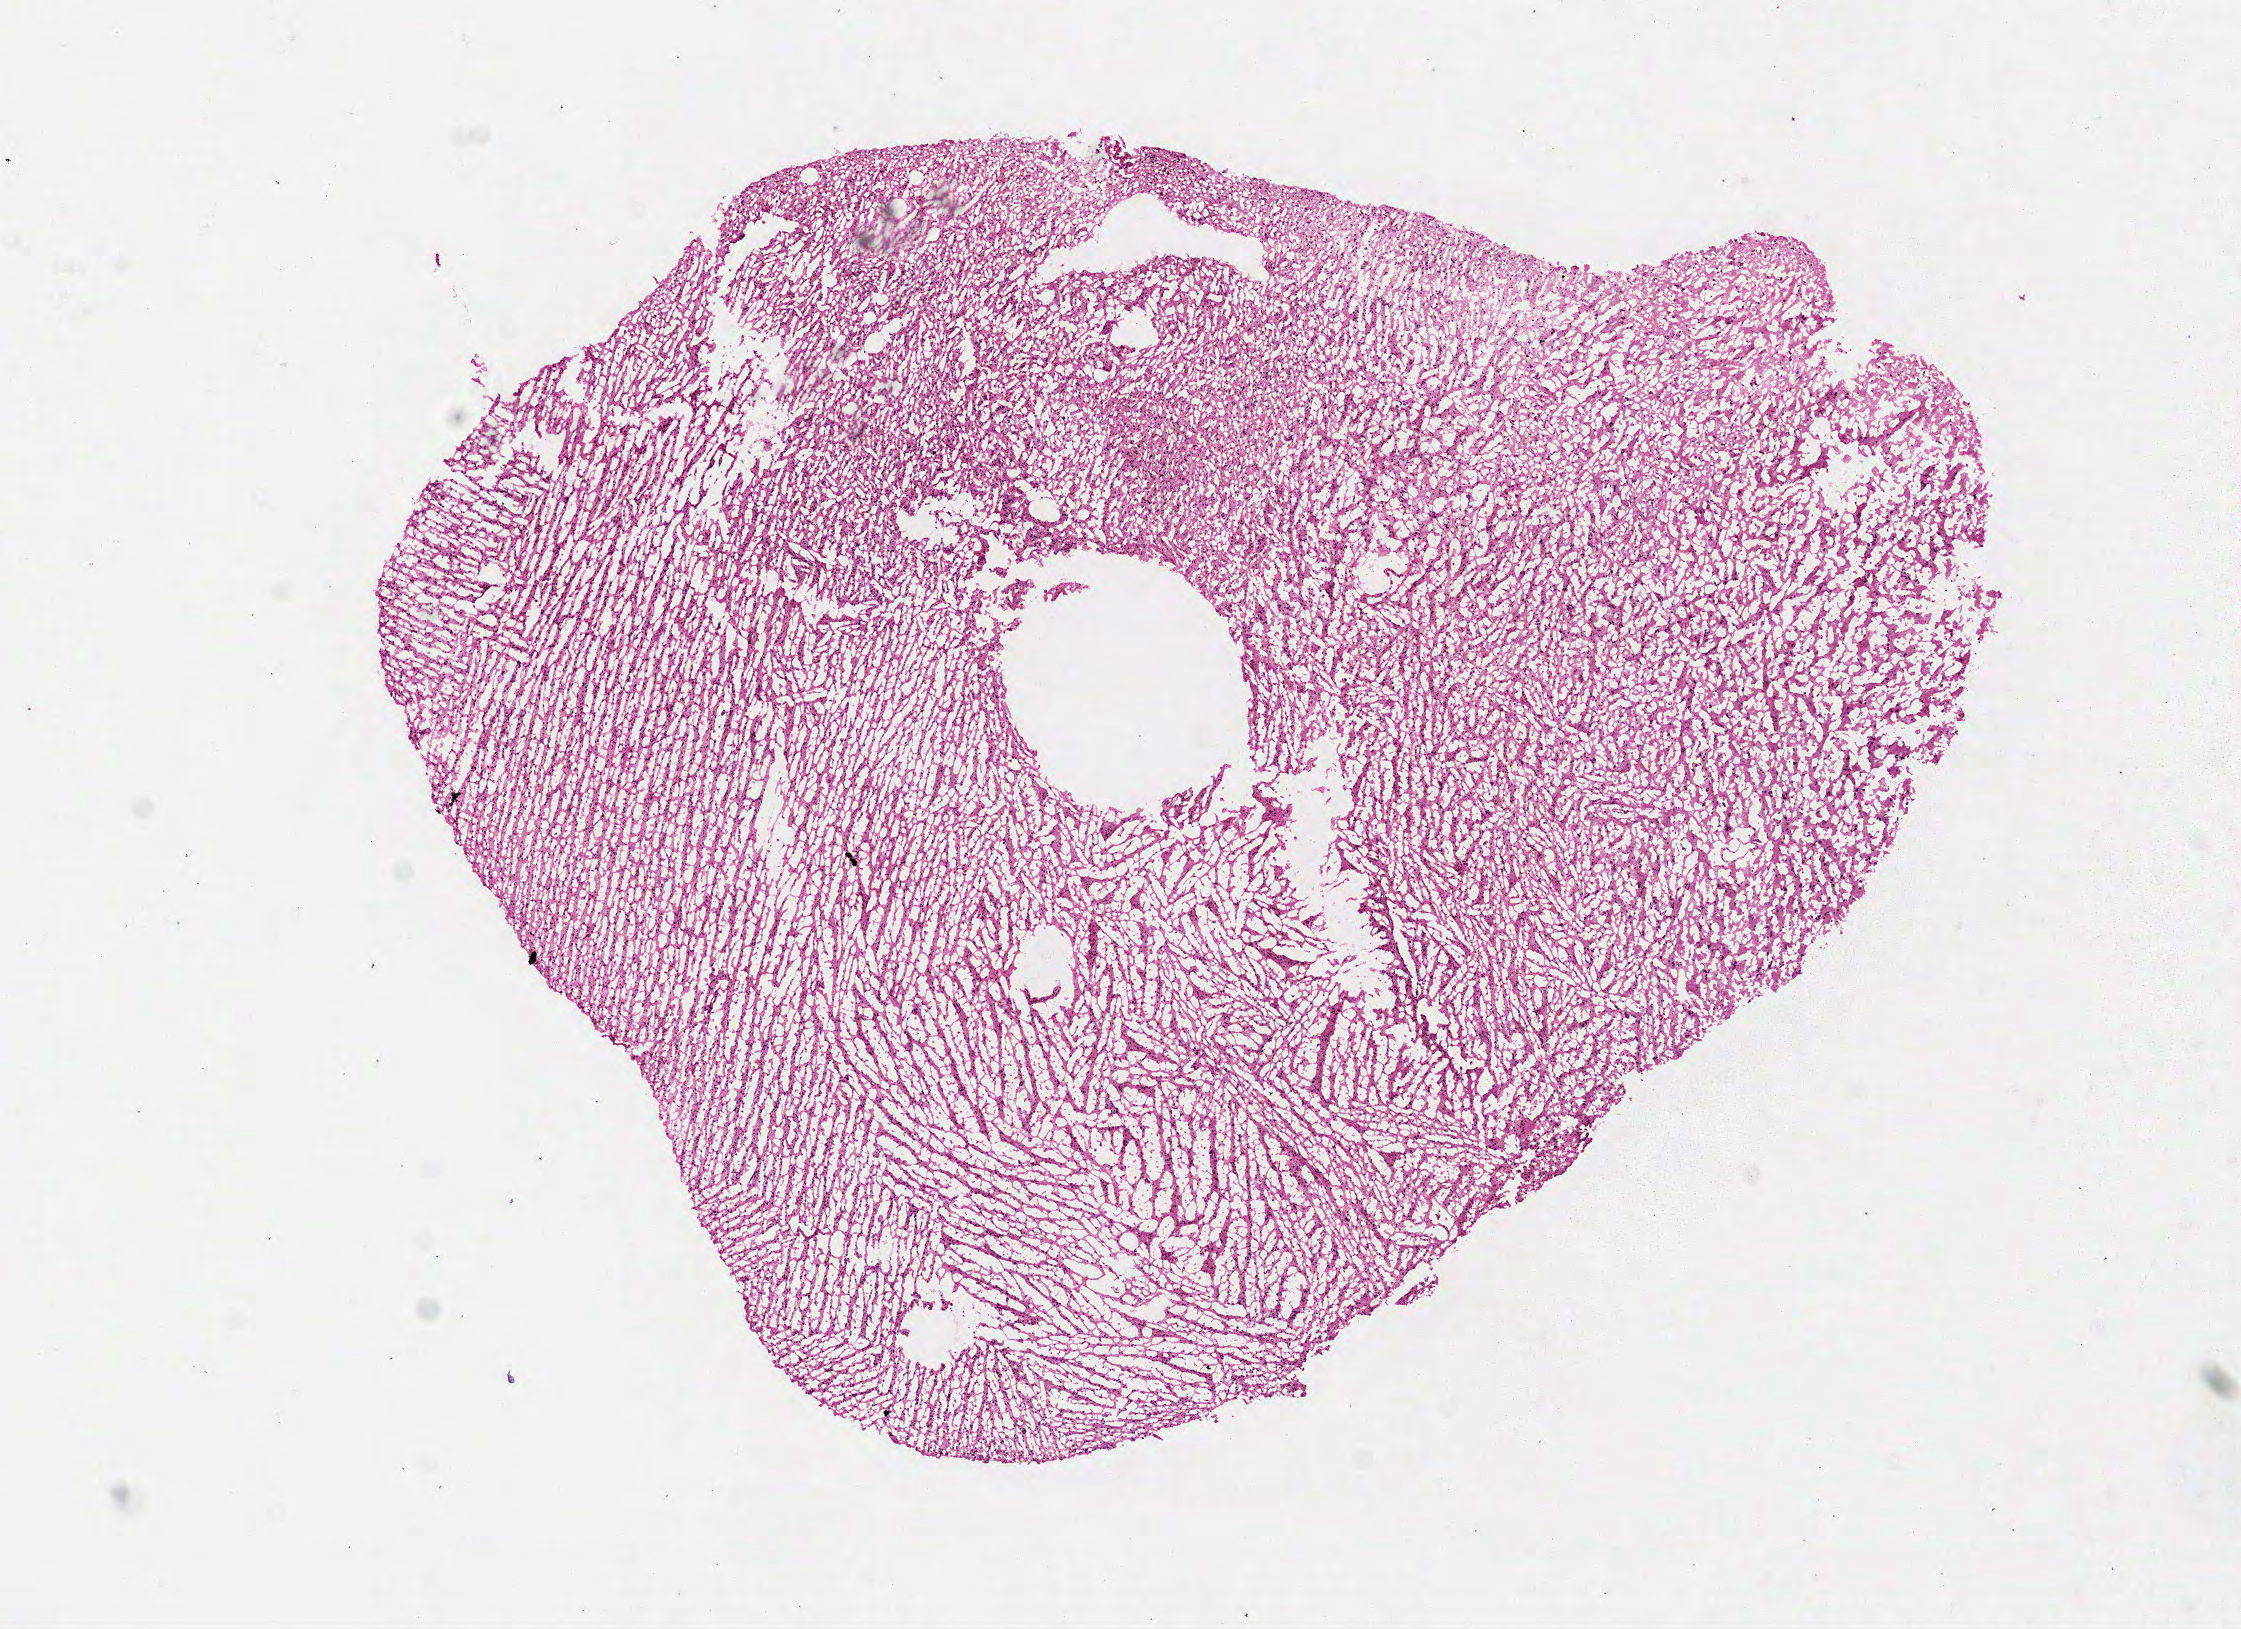
Whole-slide histology image, H&E, low-resolution overview of the scanned area, about 9.0 x 6.6 mm (slide scanned at 40x), frozen section from the top of the tissue portion, brain, primary tumour sample. Male patient; age at initial diagnosis 31 years. Histologic grade: G2 (moderately differentiated). Composition of this section per pathologist review: tumour cells 100%, tumour nuclei 75%, normal cells 0%, stromal cells 0%, necrosis 0%.
Laterality: left. Diagnosis: Oligodendroglioma, NOS.